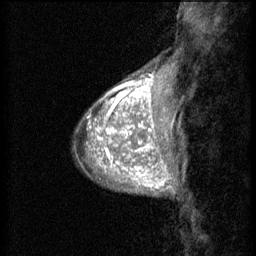
Breast MRI (dynamic contrast-enhanced), one sagittal slice; slice 13 of 60 in the series (ordered by position); 3 images stored at this slice position (order not interpretable as contrast timing); 1.5 T; TE 4.2 ms, TR 8.2 ms; 256 × 256 image matrix, field of view 180 × 180 mm. Female patient, age 38 years.
Outlined on this slice (semi-automatically segmented with operator editing):
- analysis volume of interest (the breast-tissue region the enhancement analysis was run in; not a lesion): box from (x=95, y=106) to (x=157, y=171) px
- tumour enhancement mask (voxels above the 70 % enhancement threshold inside the analysis volume of interest): (x=95, y=106)–(x=157, y=171)